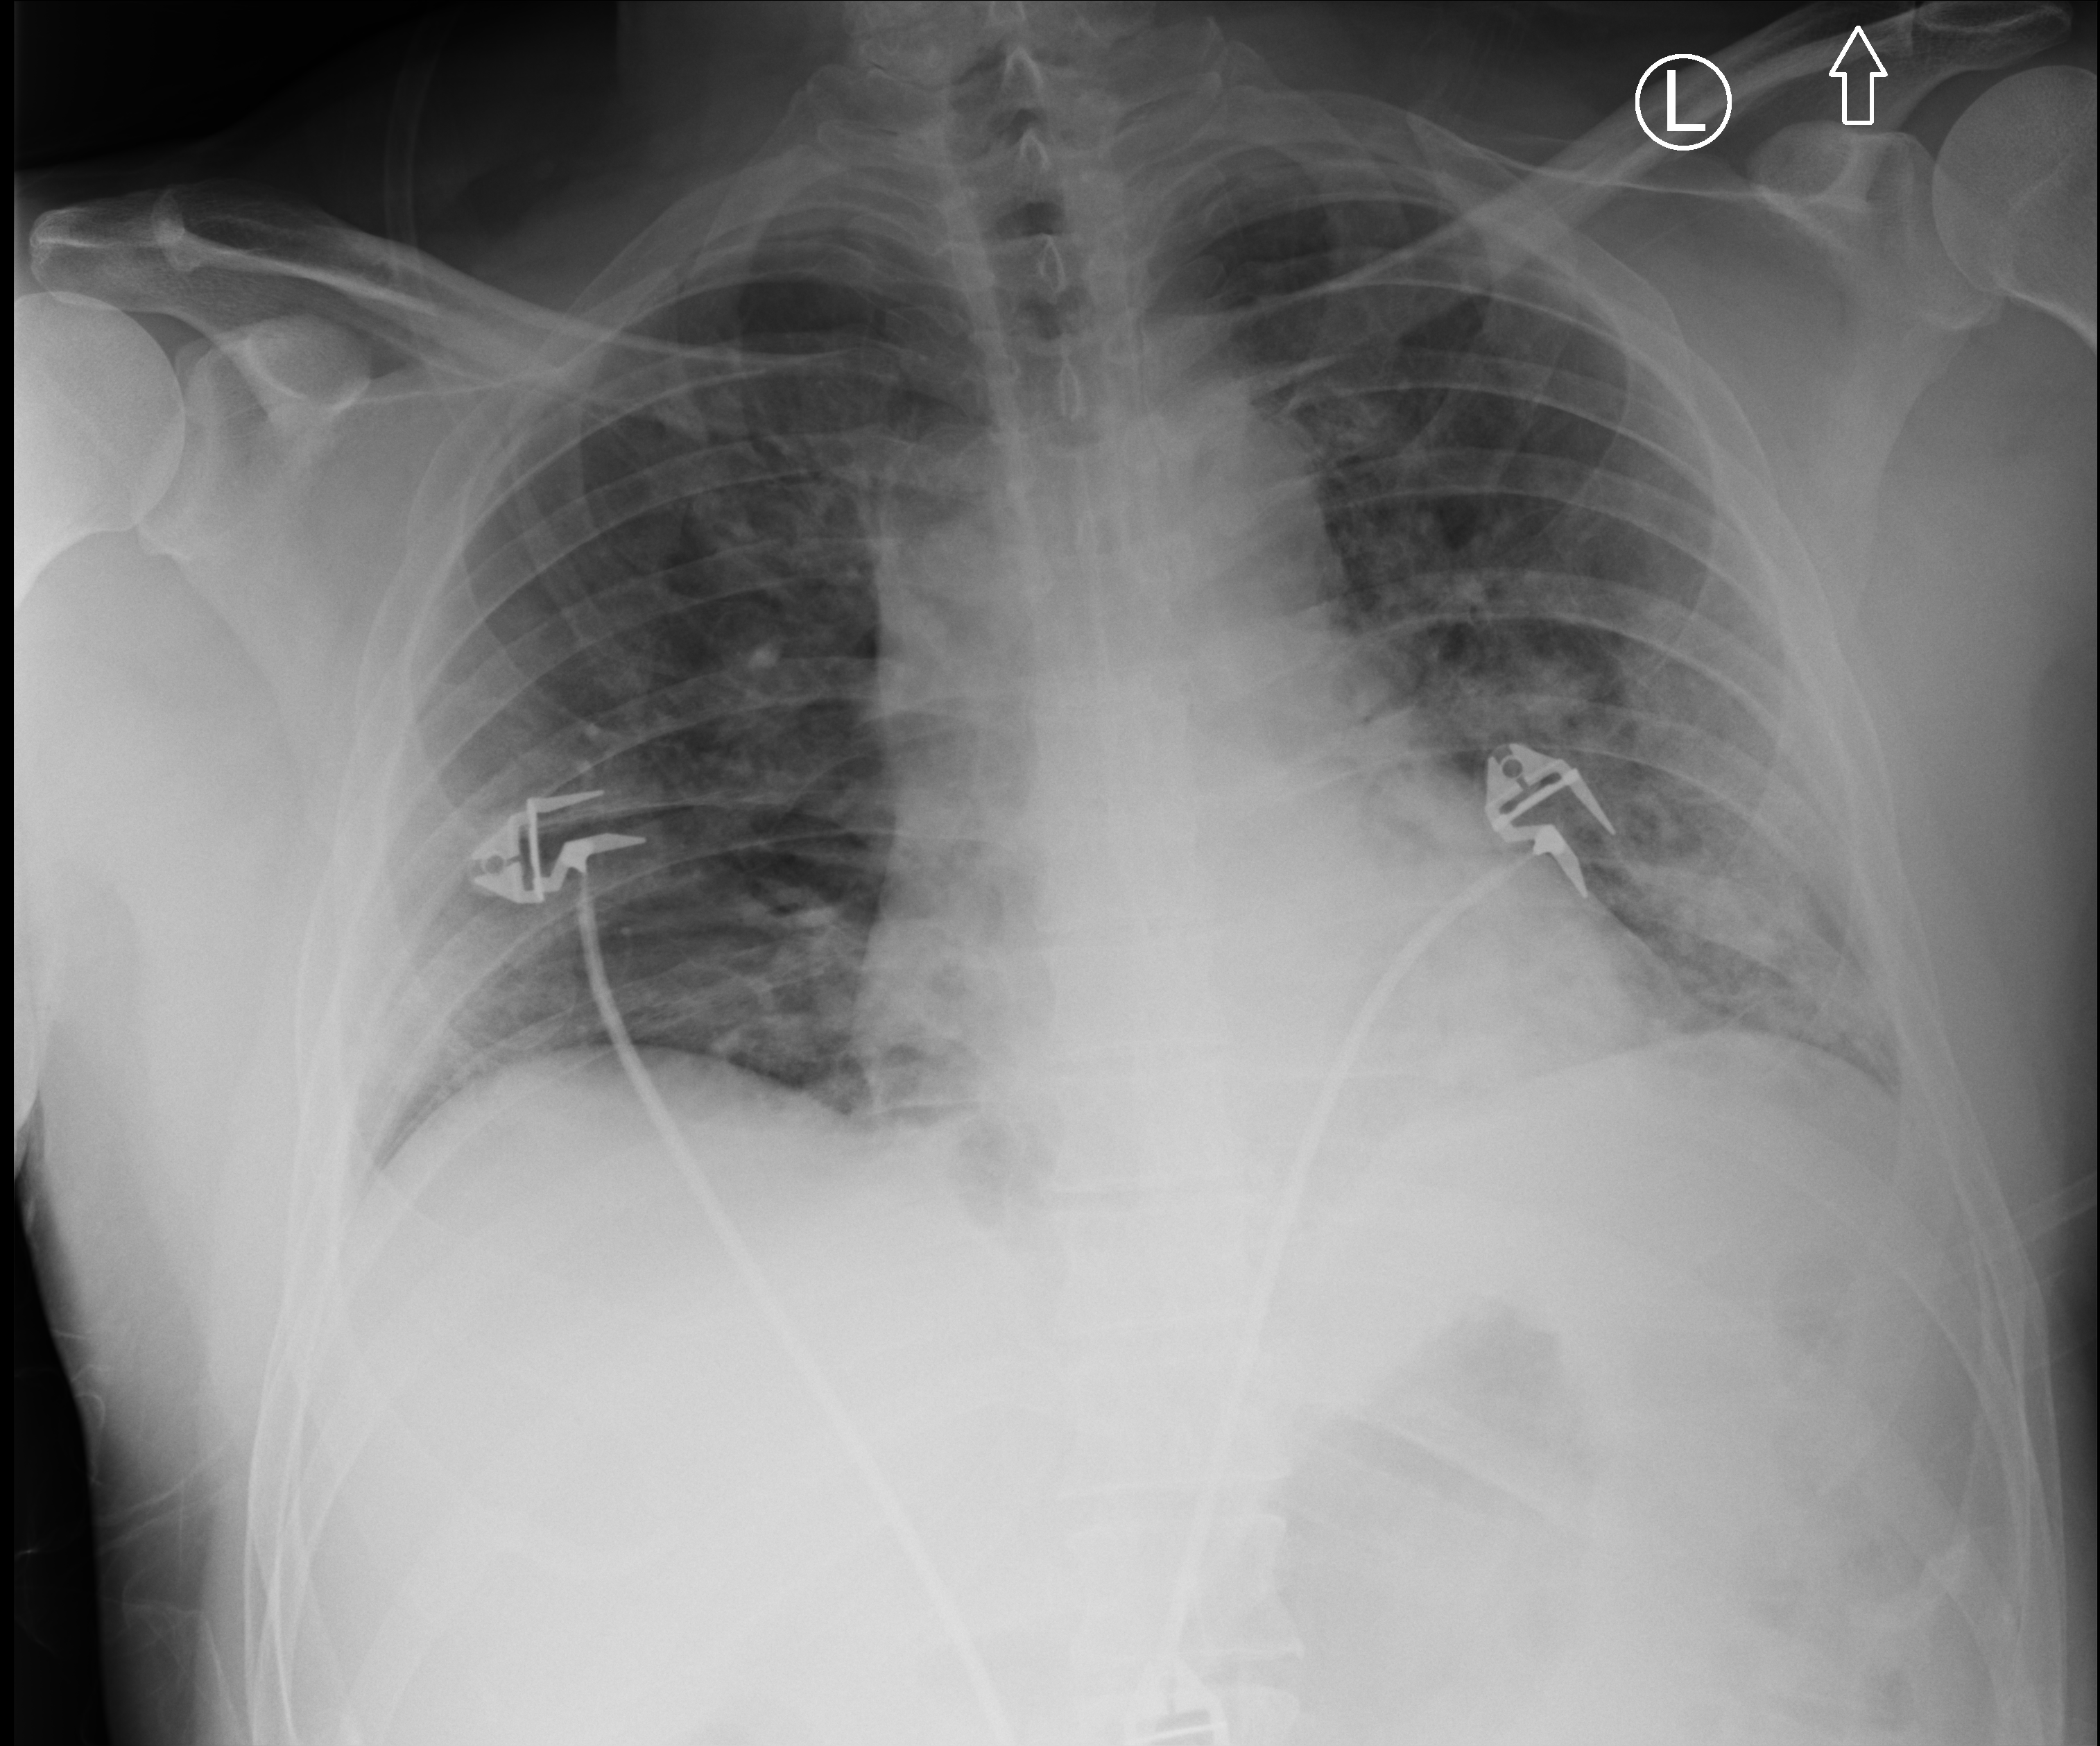
Bedside chest radiograph (computed radiography); anteroposterior (AP) projection. Patient hospitalised with COVID-19; male, aged 18–59 years.
Hospital-stay facts (about this admission, not read from this image; timing relative to this image not recorded): COPD (admission record): no; admitted to intensive care during this hospital stay: yes; chronic kidney disease (admission record): no.